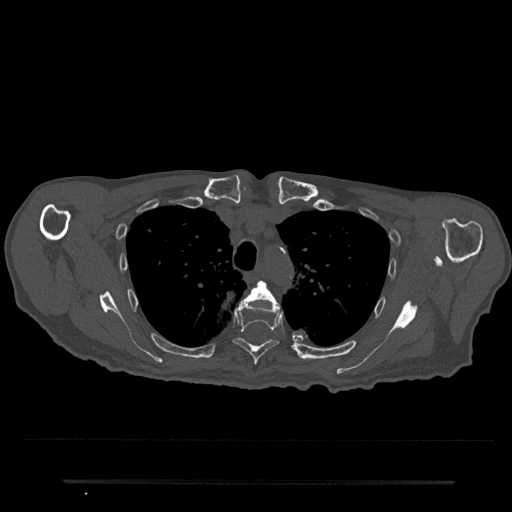
CT including the spine, one axial slice. Slice 583 of 797 in the series (ordered by position). Reconstruction kernel Br40s/3. 120 kVp. Bone window (W 1800 / L 400 HU). 0.5 mm slice thickness. 512 × 512 image matrix. Patient: male, 74 years. From the clinical record (not read from this slice): primary cancer: prostate.
Structures marked on this image (semi-automatic segmentation, software-assisted and operator-edited):
- T4 vertebra: box from (x=246, y=281) to (x=277, y=303) px
- T5 vertebra: (x=233, y=298)–(x=282, y=365)